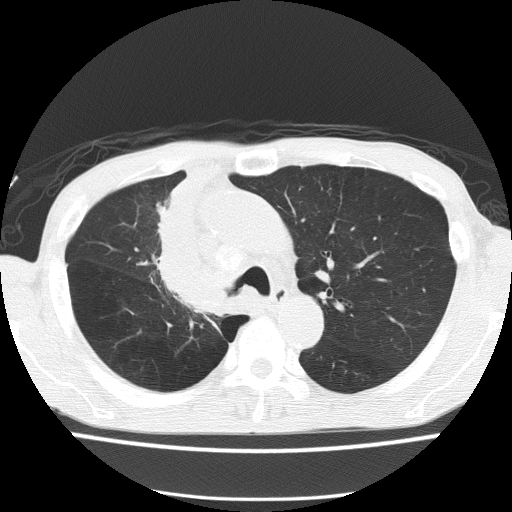
Low-dose screening chest CT, axial slice, first (baseline) screen, lung window (W 1500 / L -600 HU), 120 kVp. Male, age 59 years at enrolment. Former smoker at enrolment.
- Expert reader's lesion annotation, box from (x=137, y=232) to (x=235, y=323) px.
- The screening reader recorded 5 non-calcified nodules or masses ≥4 mm on this exam (left upper lobe, left upper lobe, left upper lobe, right middle lobe, right lower lobe); which of them this box marks is not recorded.
- Later outcome: lung cancer diagnosed 72 days after this screen — squamous cell carcinoma, NOS, right upper lobe, moderately differentiated (G2), stage IV (AJCC 6th edition).